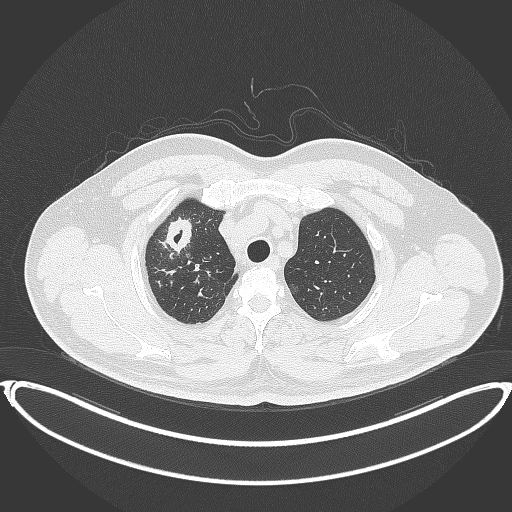
Chest CT, one axial slice; position 326 of 399 along the scan axis; lung window (W 1500 / L -600 HU); 1 mm slice thickness; 512 × 512 image matrix, field of view 445 × 445 mm. Patient: male, 53 years. Case-level facts recorded for this patient, not image findings: clinical TNM (as recorded): T2a N0 M0.
Structures marked on this image (rectangle marked by the reading radiologist):
- lung tumour (recorded histology: adenocarcinoma): bounding box [x1, y1, x2, y2] px = [163, 214, 200, 255]